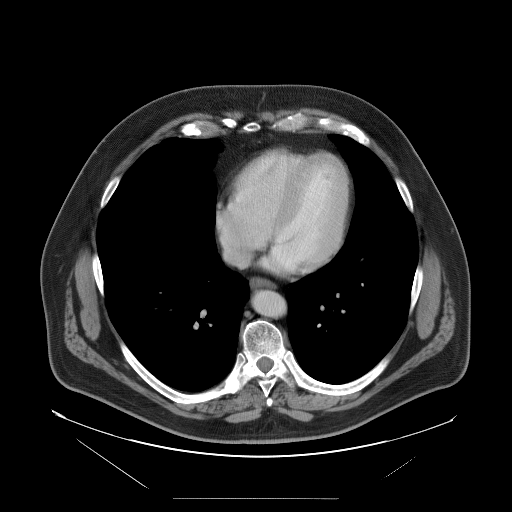
Contrast-enhanced abdominal CT, one axial slice; position 103 of 114 along the scan axis; 120 kVp; intravenous contrast given; soft-tissue window (W 400 / L 40 HU); 5 mm slice thickness; 512 × 512 image matrix, field of view 500 × 500 mm. Male patient, age 61 years. Case-level facts recorded for this patient, not image findings: diagnosis: colorectal cancer liver metastases, imaged before liver resection; multiple liver metastases: no; largest metastasis: 6.5 cm; disease in both lobes: yes.
Structures marked on this image (expert manual segmentation):
- hepatic veins: bounding box <218,214,268,267> (left, top, right, bottom; pixels)